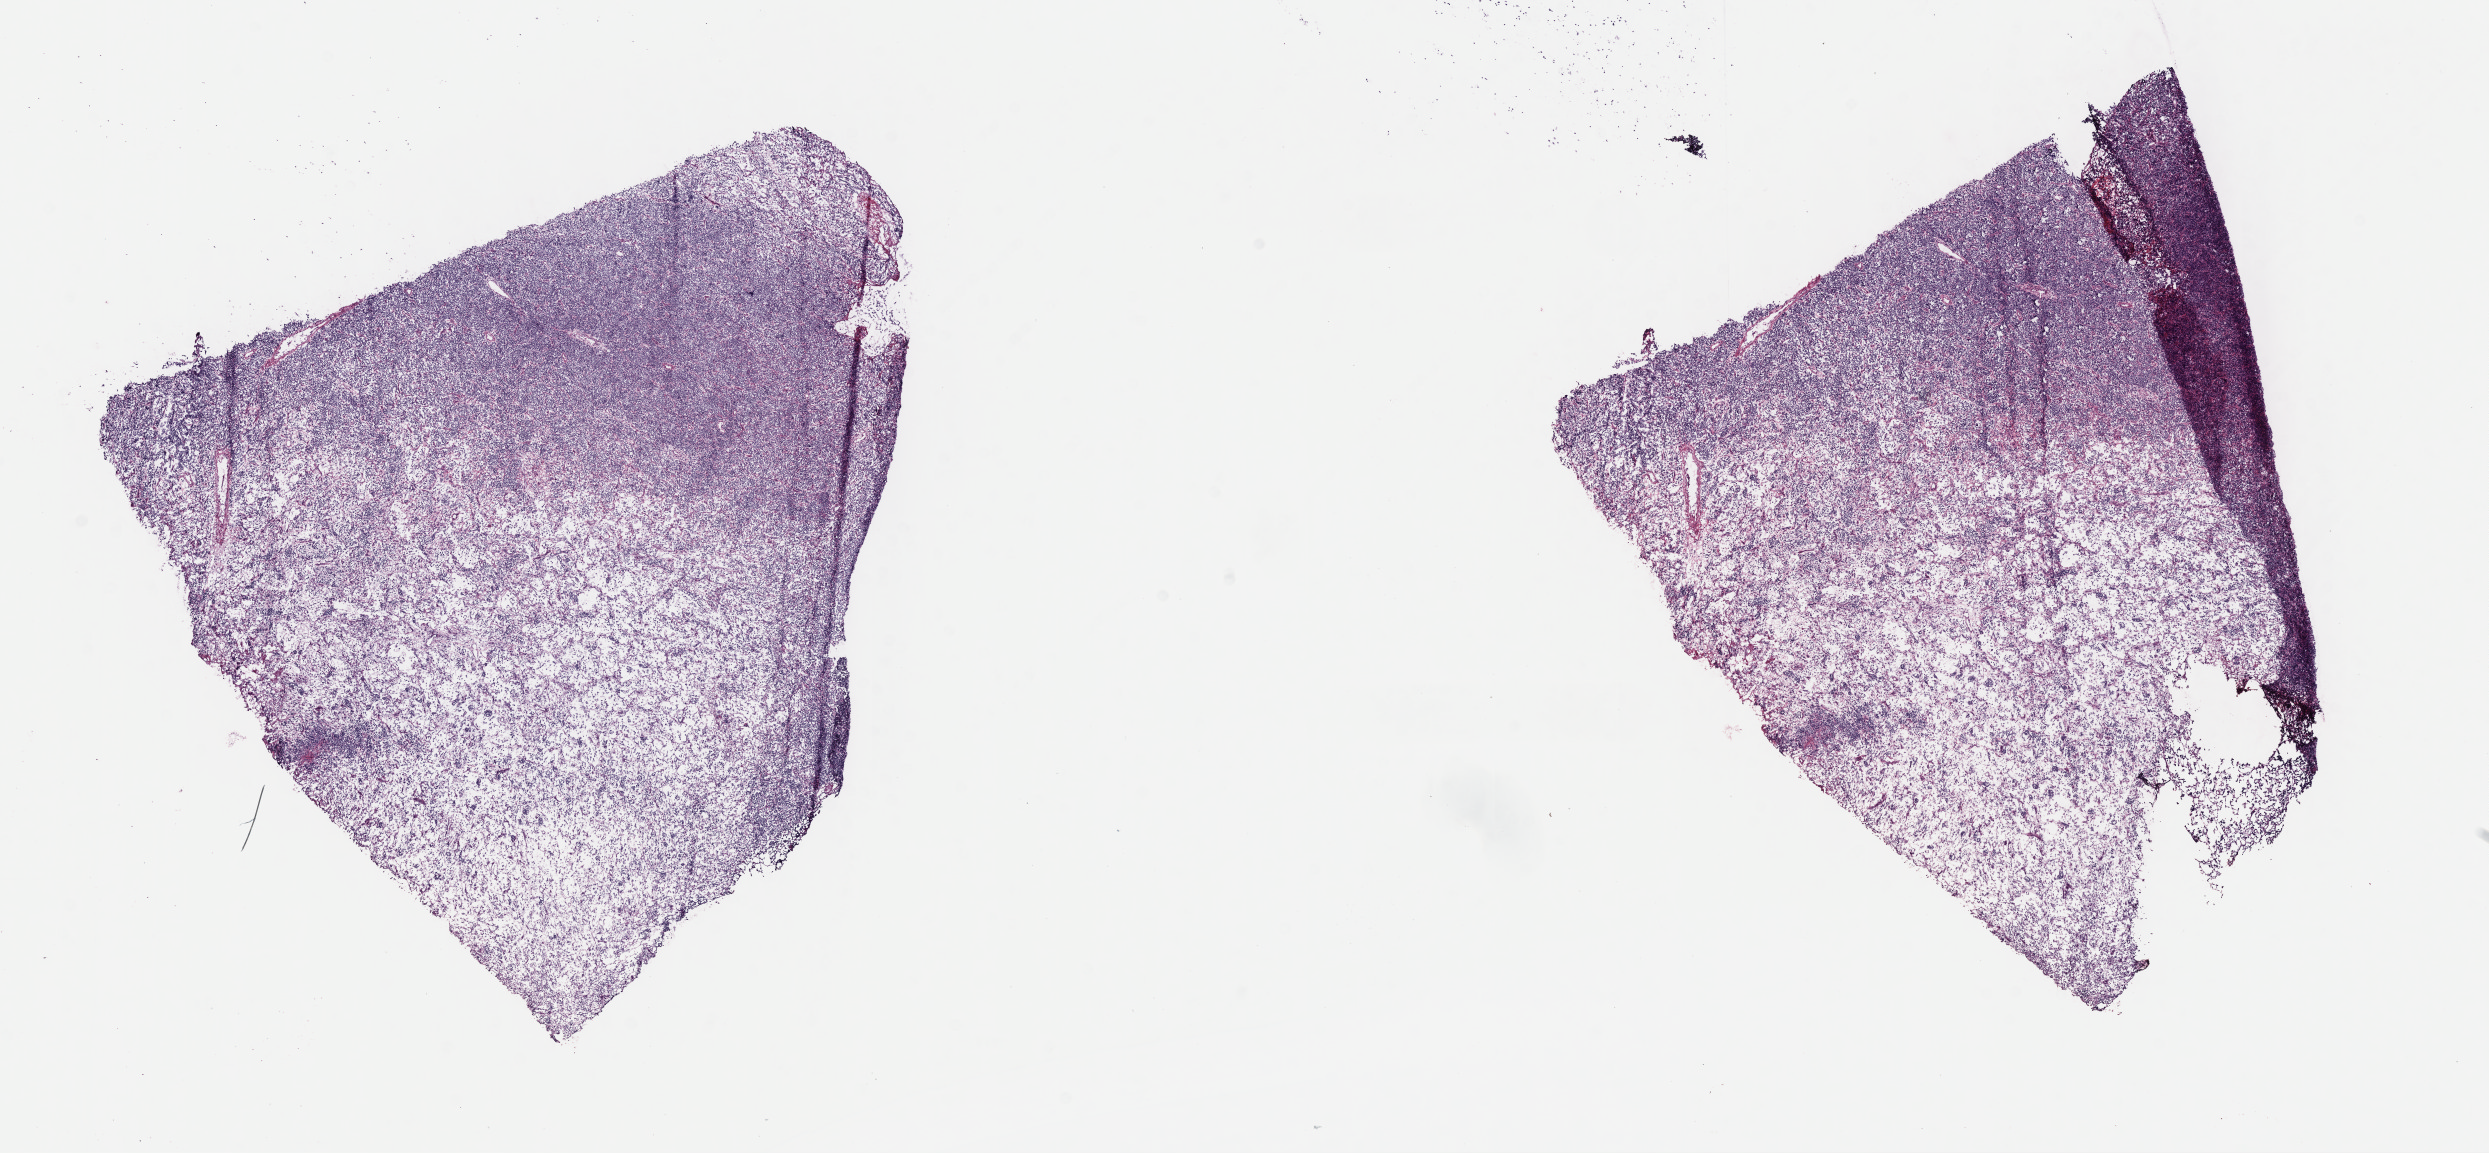
H&E whole-slide image — shown as a low-resolution overview of the whole scanned area (about 20.1 x 9.3 mm), cryosection, primary tumor, anatomic site: cranium. Male, age 5 years at initial diagnosis. Pathologist review of this section (percent, as recorded): tumor cells 93%, tumor nuclei 90%, stromal cells 5%, necrosis 2%, normal cells 0%. Infiltration values recorded for this section: lymphocyte infiltration 3%, monocyte infiltration 3%, neutrophil infiltration 0%.
* section: top of the tissue portion
* Ann Arbor stage (patient): Stage III
* histologic diagnosis: Burkitt lymphoma, NOS